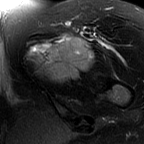
MRI of an extremity soft-tissue mass, one axial slice. Slice 48 of 60 in the series (ordered by position). T2-weighted fat-saturated. MR volume resampled by the dataset authors to the PET/CT grid (not the native acquisition matrix). 3.27 mm slice thickness. 144 × 144 image matrix, field of view 141 × 141 mm. Female patient. Case-level facts recorded for this patient, not image findings: histological type: pleiomorphic leiomyosarcoma; grade: intermediate; site of the primary tumour: left thigh.
Structures marked on this image (expert contour drawn on MRI and transferred to this co-registered scan by the dataset authors):
- gross tumour volume including surrounding oedema: bounding box [x1, y1, x2, y2] px = [25, 33, 92, 84]
- gross tumour volume (mass): [43, 37, 92, 82]